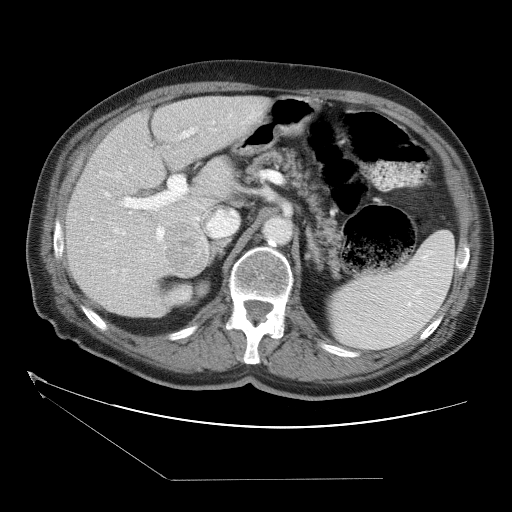
Contrast-enhanced abdominal CT (liver protocol), one axial slice; slice 19 of 38 in the series (ordered by position); 120 kVp; one of 2 acquisitions stored at this slice position; soft-tissue window (W 400 / L 40 HU); 5 mm slice thickness; 512 × 512 image matrix. From the clinical record (not read from this slice): diagnosis: hepatocellular carcinoma (patient treated with transarterial chemoembolisation; whether this scan precedes or follows treatment is not stated here); TNM stage (as recorded): Stage-II; Child-Pugh class: A; tumour differentiation: moderately differentiated; tumour nodularity: multinodular.
Annotated regions visible in this slice (semi-automatic segmentation, software-assisted and operator-edited):
- liver parenchyma outside the tumour (the mass and vessels are separate outlines, so this box may not span the whole liver): bounding box (x1, y1, x2, y2) in pixels: (66, 96, 270, 318)
- mass: (164, 221, 210, 278)
- liver vessels: (87, 121, 215, 296)